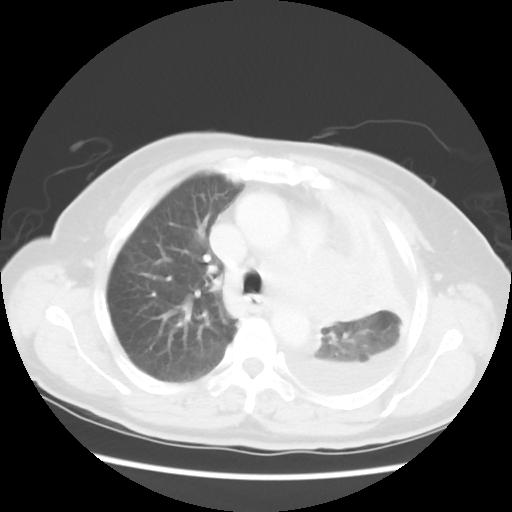
Chest CT, one axial slice. Slice 37 of 52 in the series (ordered by position). Reconstruction kernel STANDARD. 120 kVp. Lung window (W 1500 / L -600 HU). 5 mm slice thickness. 512 × 512 image matrix, field of view 336 × 336 mm. Female patient, age 72 years. Case-level facts recorded for this patient, not image findings: clinical TNM (as recorded): T4 N3 M1b; histopathological grade: G3.
Structures marked on this image (bounding box drawn by a radiologist):
- lung tumour (recorded histology: large cell carcinoma): bounding box <293,242,382,337> (left, top, right, bottom; pixels)